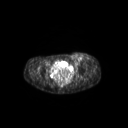
FDG PET of an extremity soft-tissue mass (from a PET/CT study), one axial slice; slice 75 of 267 in the series (ordered by position); 3.27 mm slice thickness; 128 × 128 image matrix. Female patient, age 24 years. From the clinical record (not read from this slice): histological type: leiomyosarcoma; grade: high; site of the primary tumour: groin.
Annotated regions visible in this slice (expert contour drawn on MRI and transferred to this co-registered scan by the dataset authors):
- gross tumour volume including surrounding oedema: bounding box [x1, y1, x2, y2] px = [70, 53, 92, 64]
- gross tumour volume (mass): [70, 53, 82, 63]